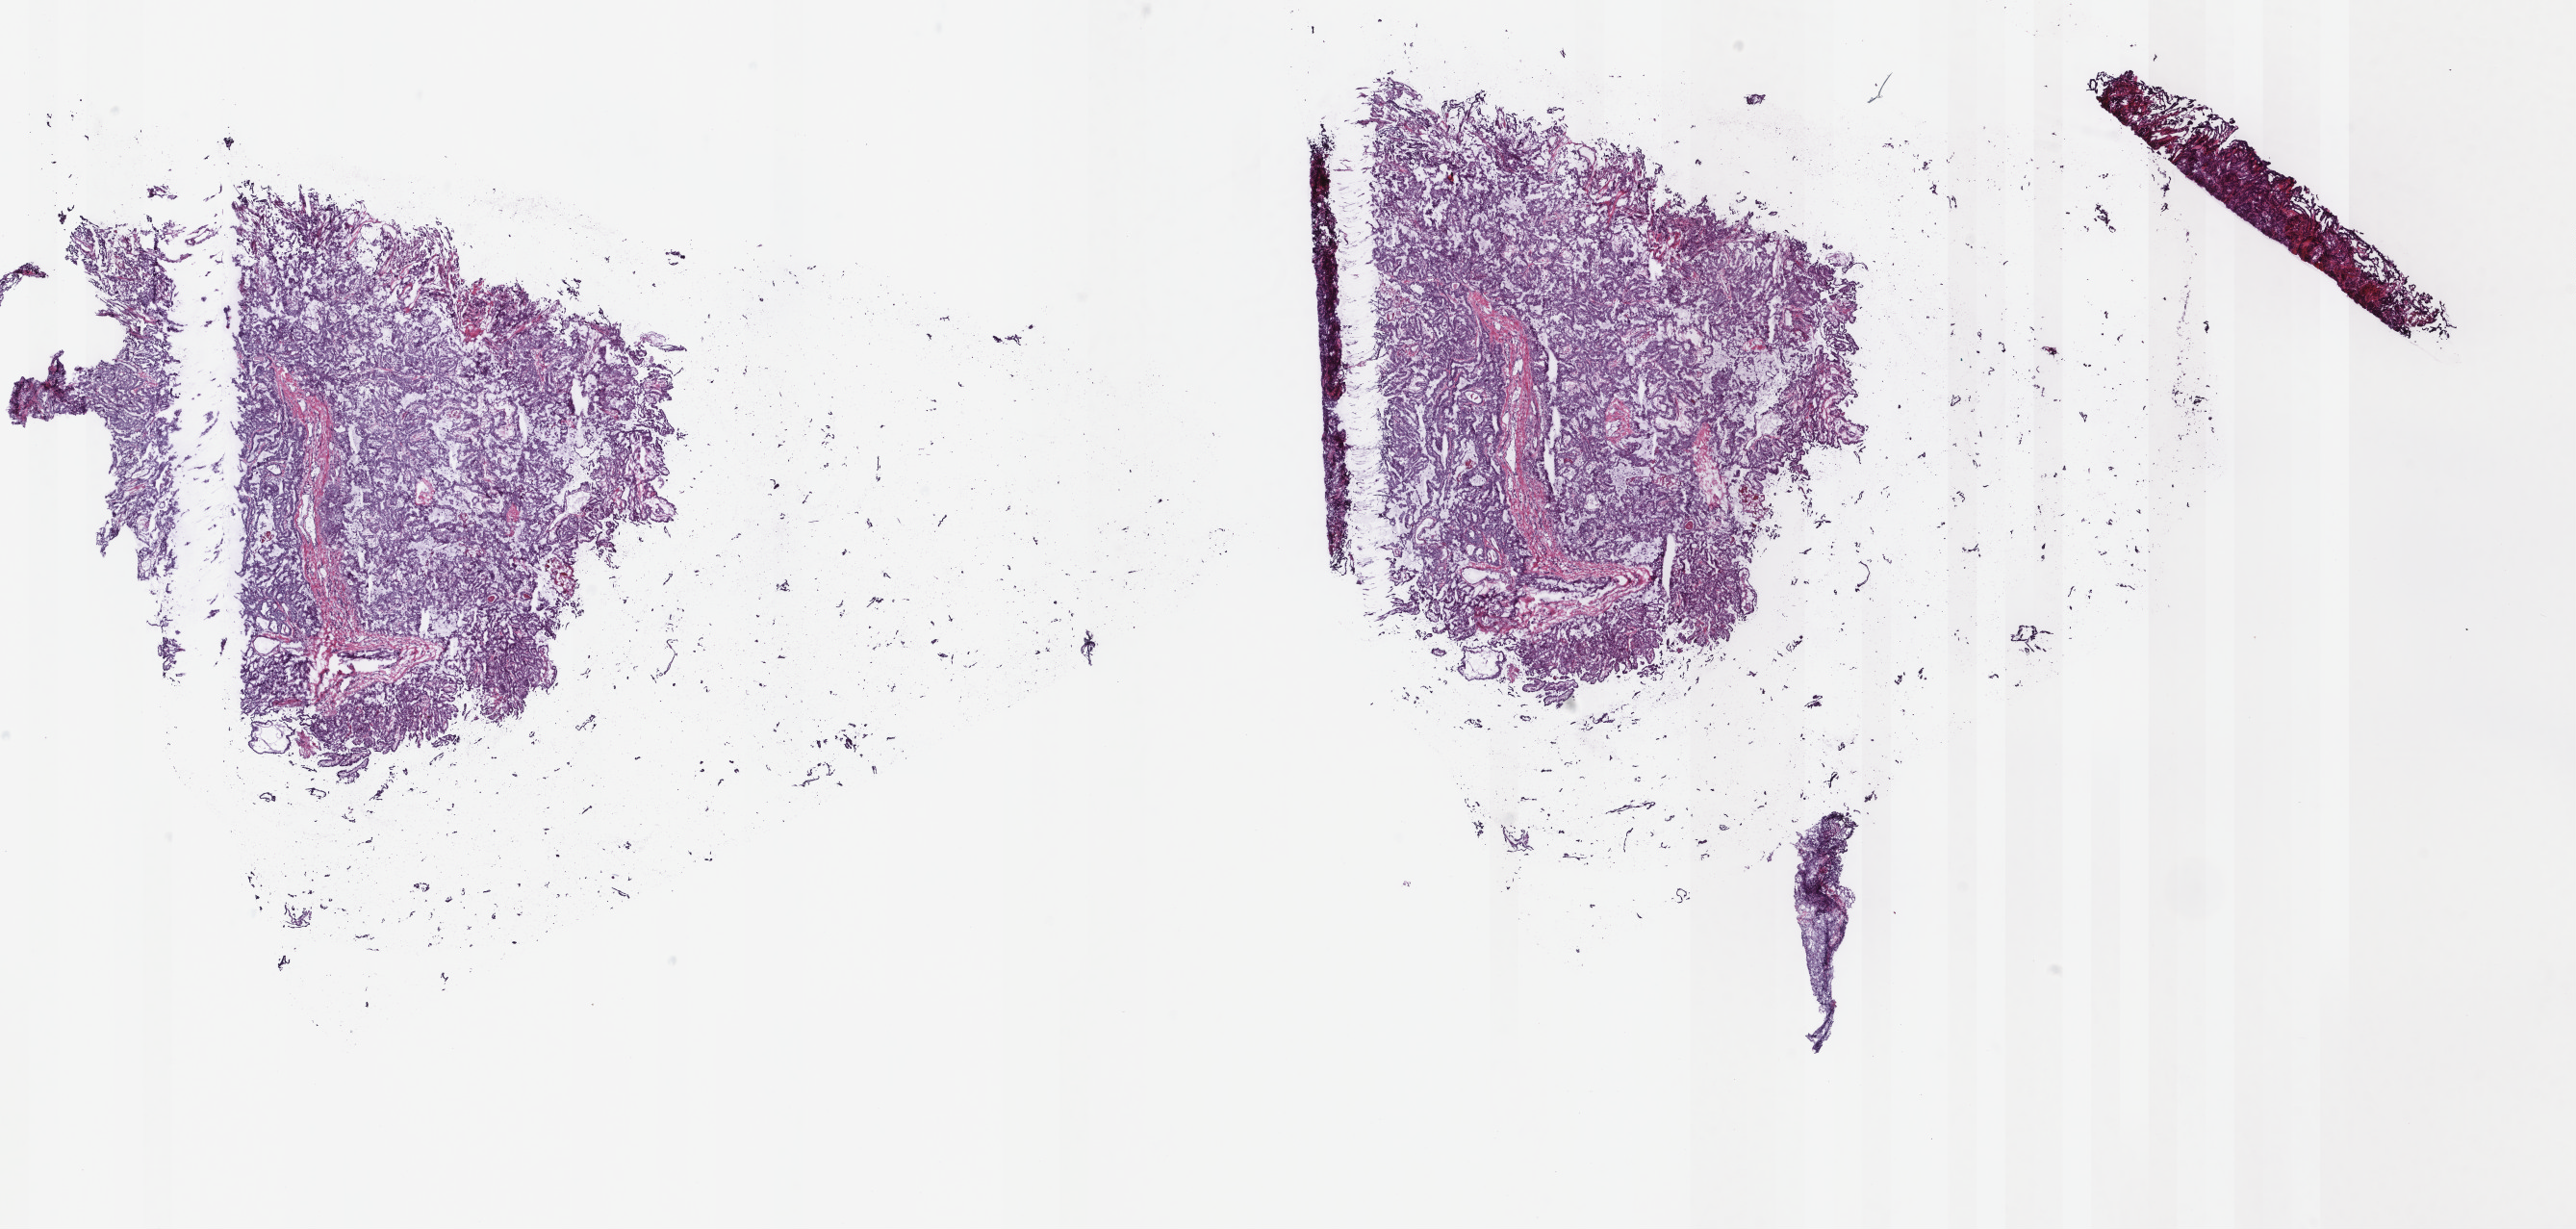
H&E-stained whole-slide image, shown as a low-resolution overview of the whole scanned area (about 21.2 x 10.1 mm), frozen section from the top of the tissue portion, primary tumour sample from the thyroid. Patient: female, age at initial diagnosis 30 years. Slide review estimates, as recorded: tumour cells 95%, tumour nuclei 95%, normal cells 0%, stromal cells 5%, necrosis 0%. Inflammatory infiltration, as recorded: lymphocyte infiltration 0%, monocyte infiltration 0%, neutrophil infiltration 0%.
- AJCC pathologic stage: I
- pathologic diagnosis: Papillary adenocarcinoma, NOS (thyroid gland)
- lymph nodes positive (case pathology): 9 of 14 examined